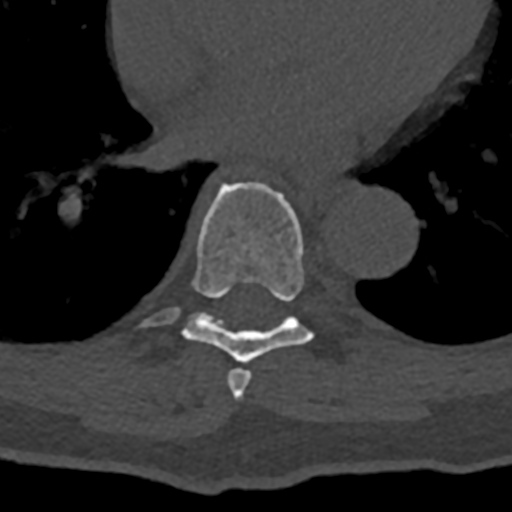
CT including the spine, one axial slice; slice 707 of 797 in the series (ordered by position); reconstruction kernel Br40s/3; bone window (W 1800 / L 400 HU); 0.5 mm slice thickness; 512 × 512 image matrix. Patient: male, 74 years. From the clinical record (not read from this slice): primary cancer: renal.
Annotated regions visible in this slice (semi-automatically segmented with operator editing):
- T7 vertebra: bounding box <227,368,251,400> (left, top, right, bottom; pixels)
- T8 vertebra: <141,182,320,363>